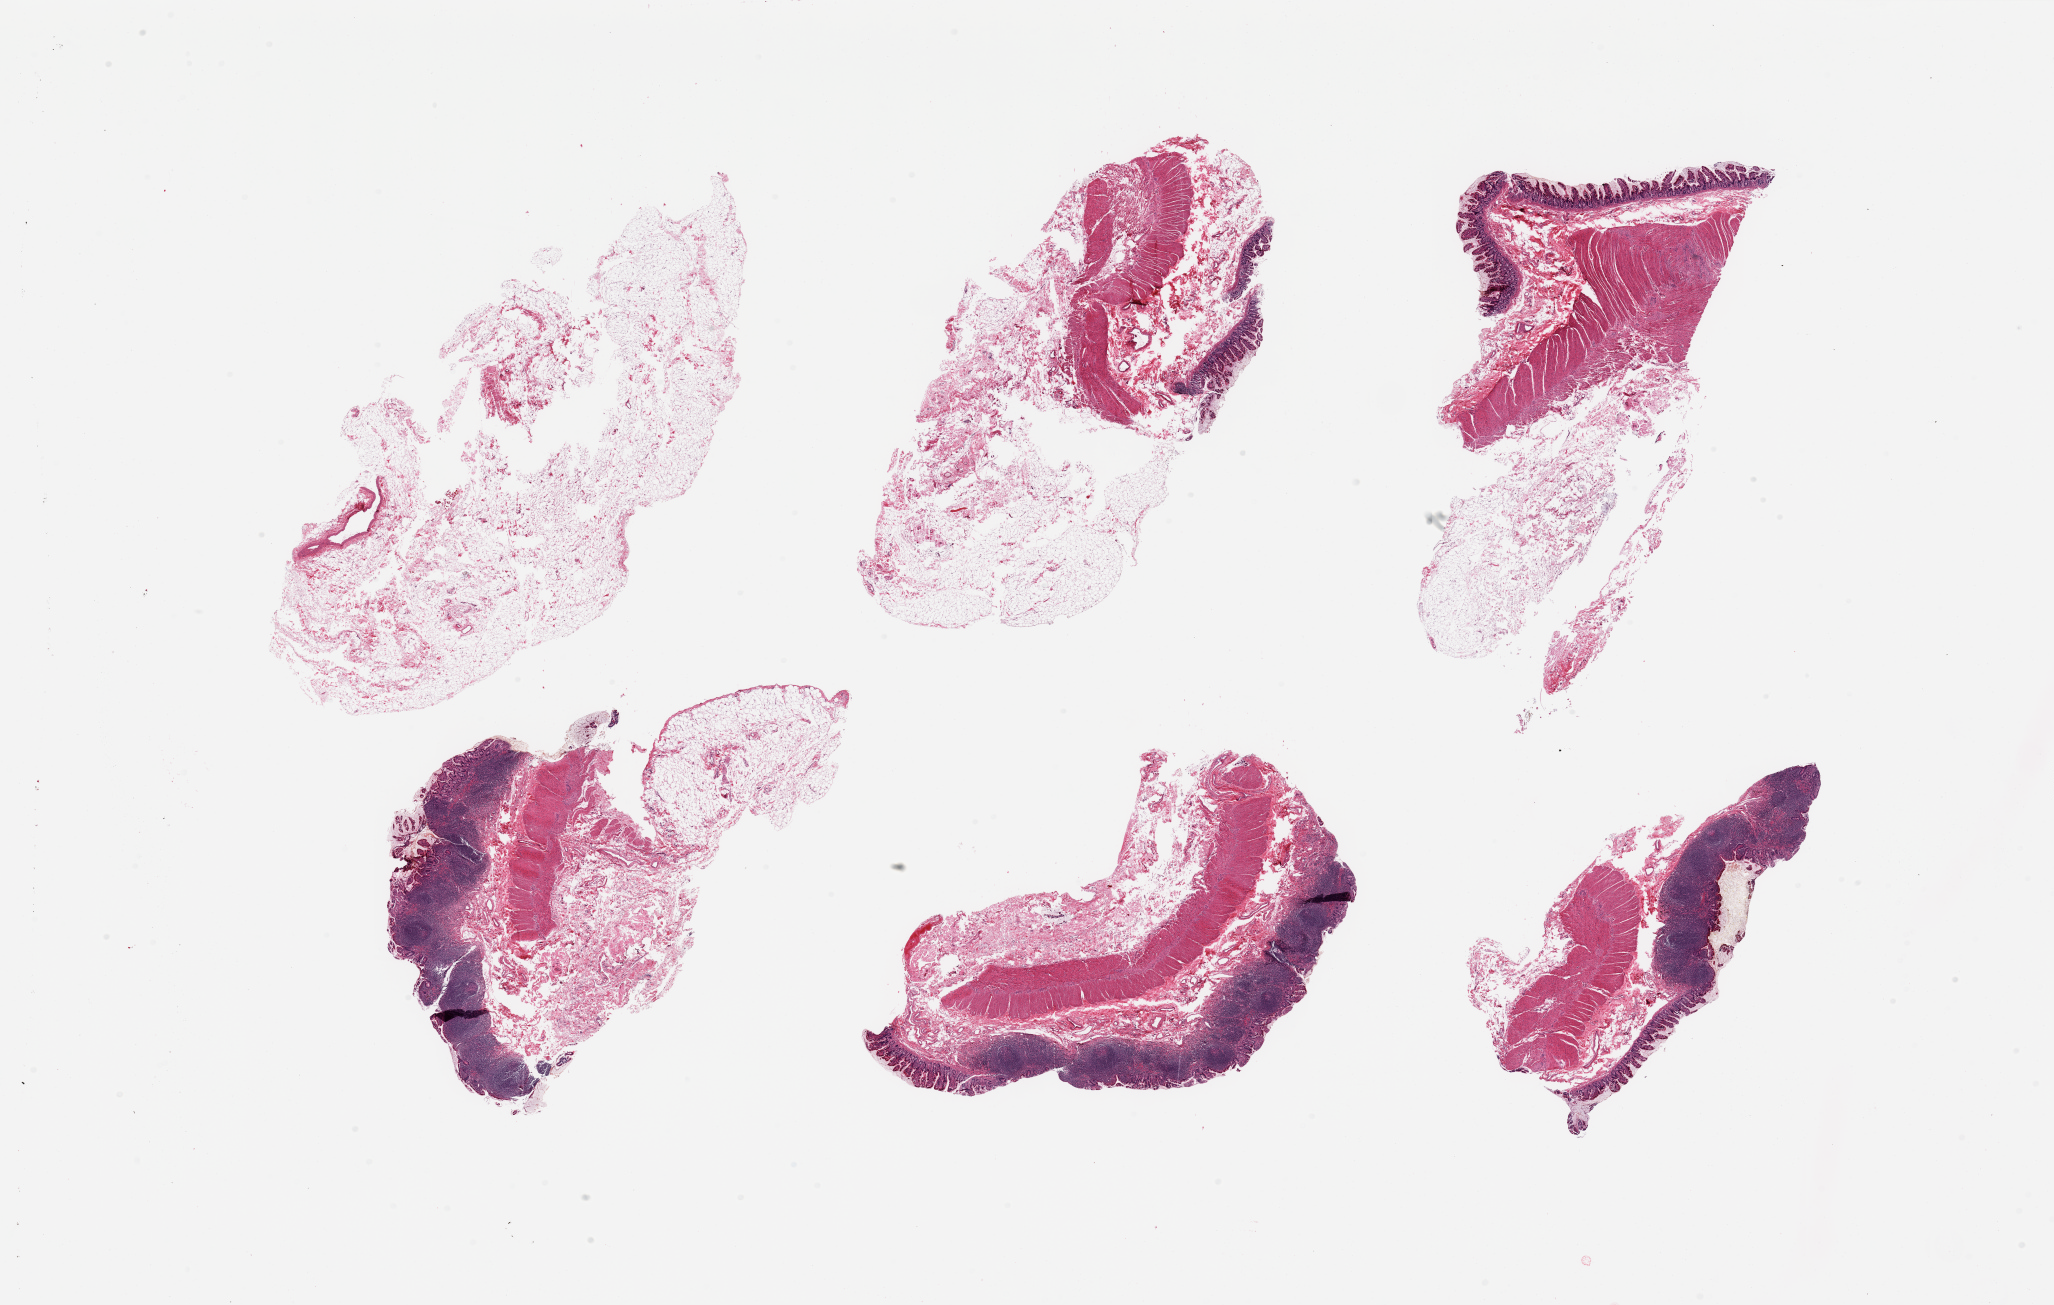
Hematoxylin and eosin (H&E) whole-slide image, whole scanned area (about 32.5 x 20.6 mm, slide scanned at 20x) shown as a low-resolution overview. PAXgene-fixed paraffin-embedded (PFPE) section. Section of ileum (target tissue). Tissue donor sample. Donor sex: female.
Reviewer comment on this tissue sample: 6 pieces, well-defined lymphoid aggregates, ~20% of tissue.